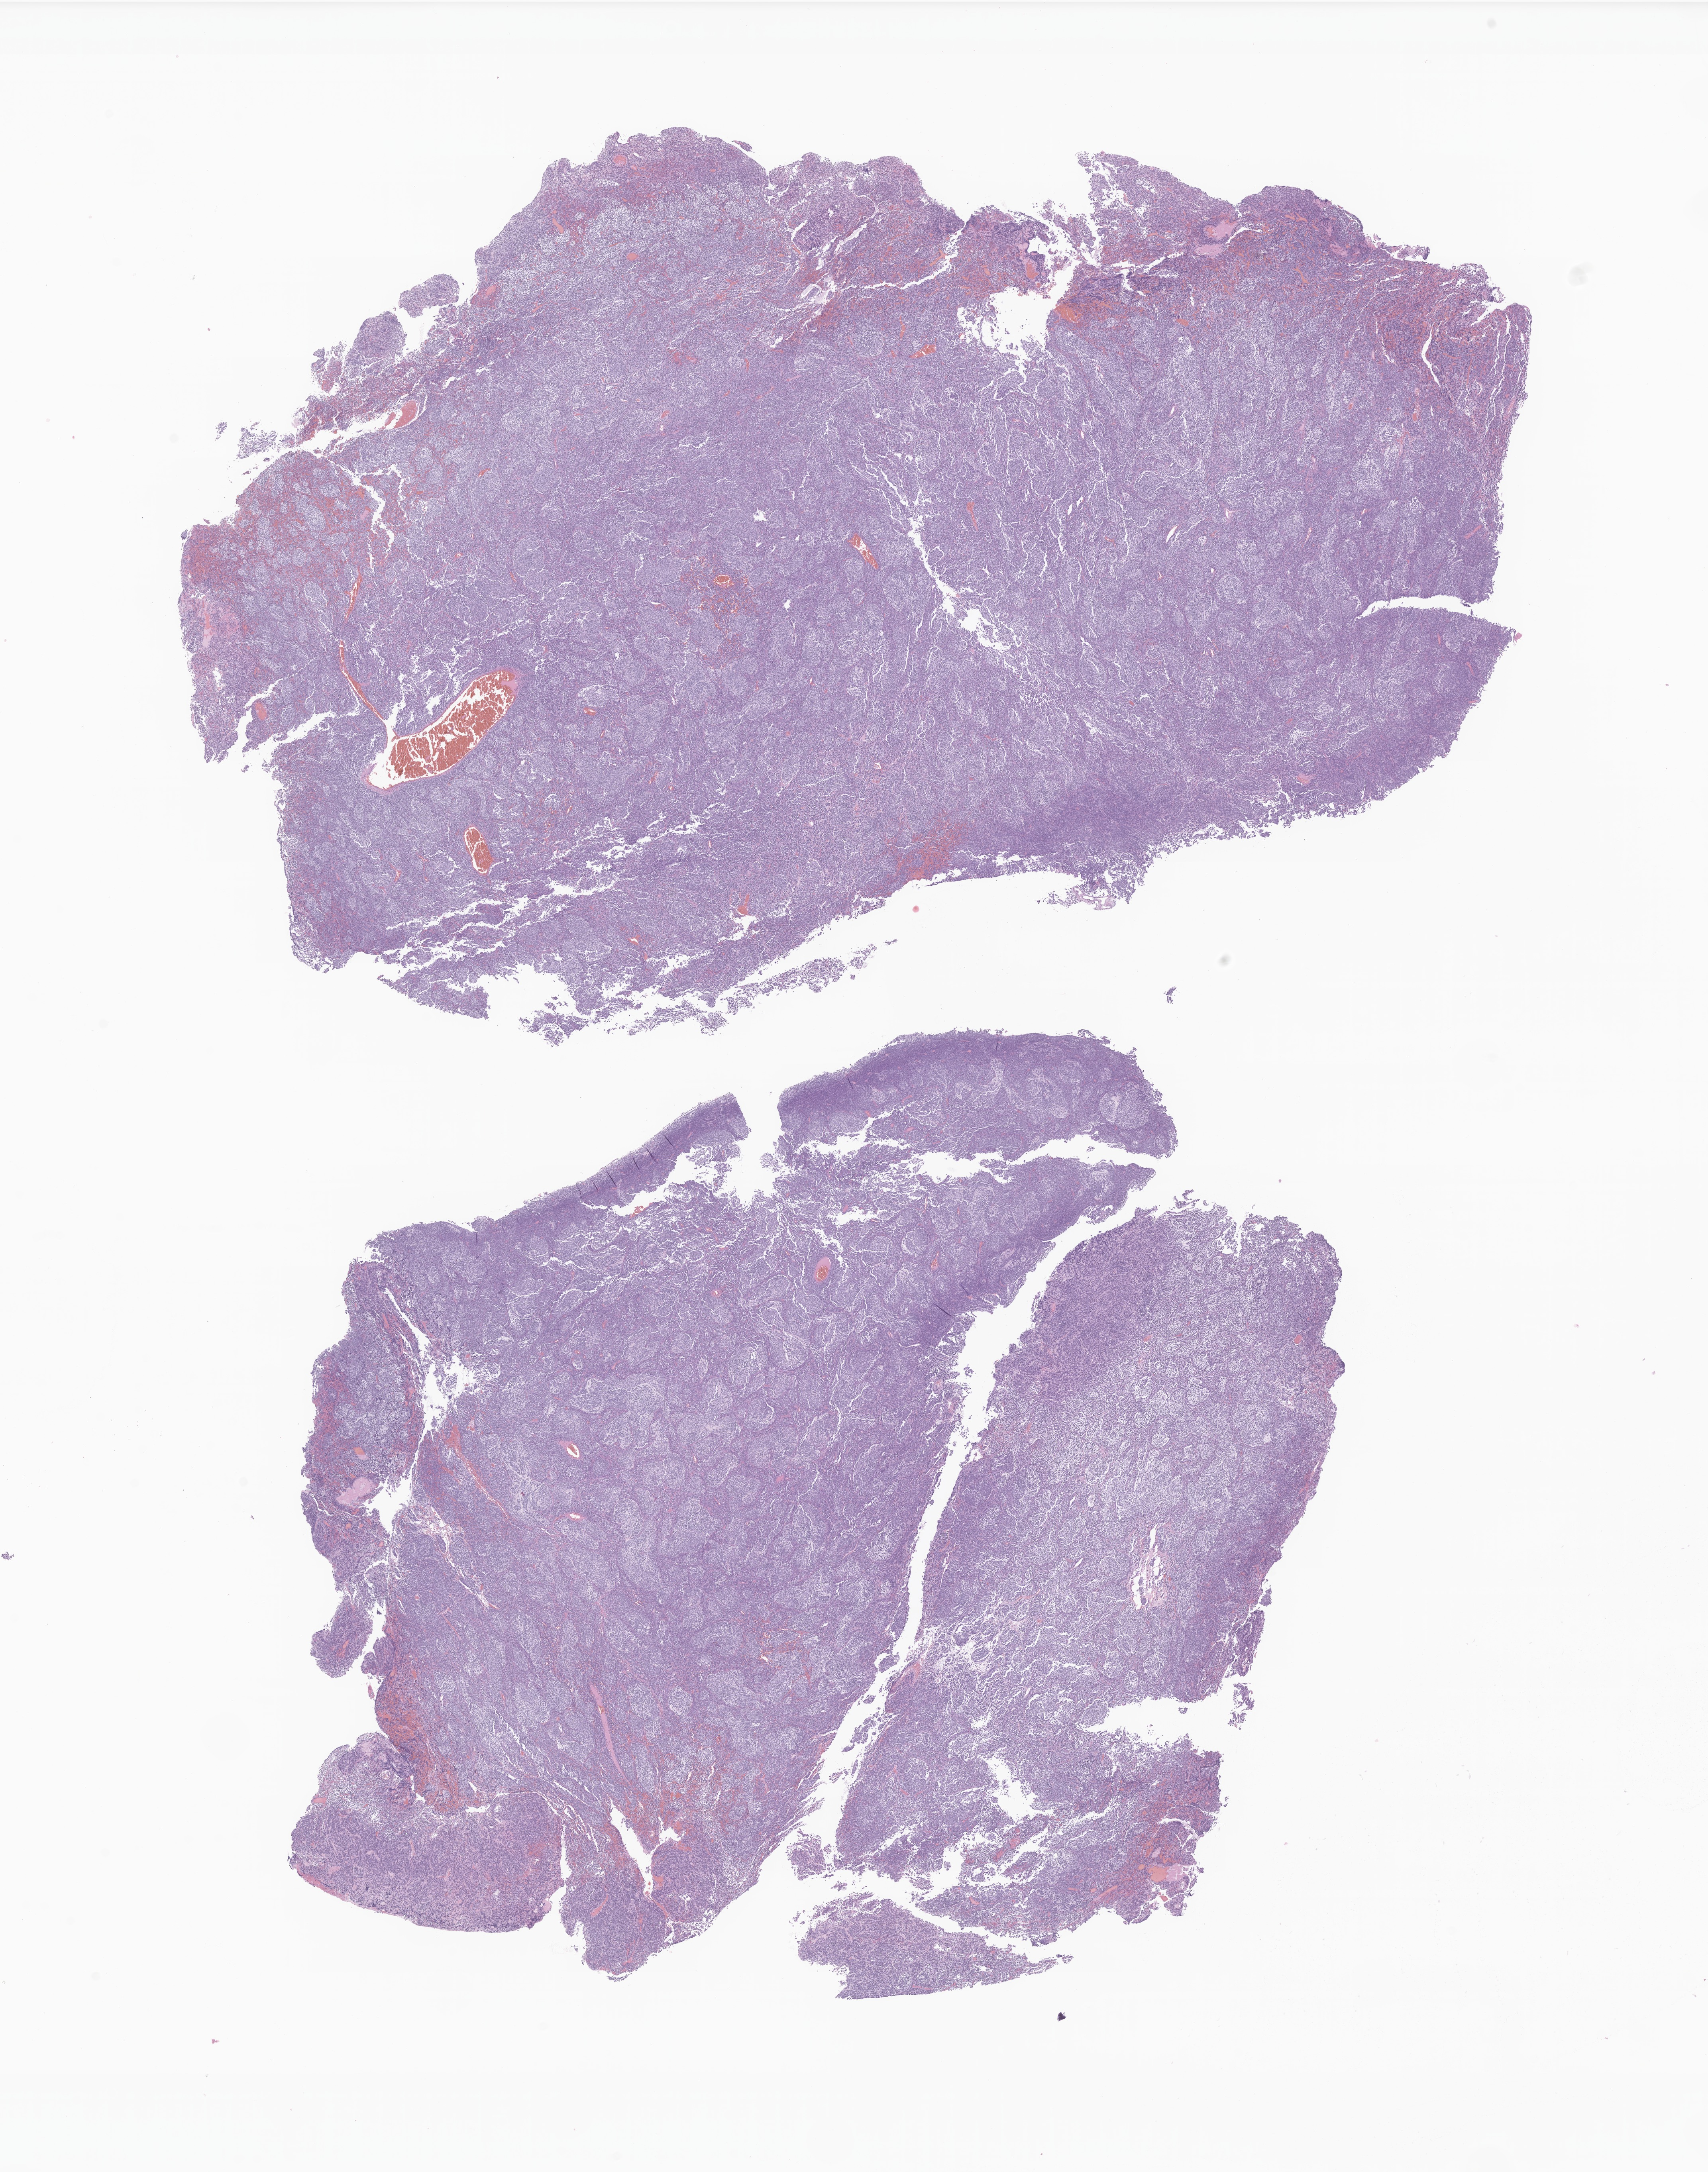
Hematoxylin and eosin (H&E) whole-slide image of tumor tissue from the brain, shown as a low-resolution overview of the whole scanned area (about 18.1 x 23.0 mm), FFPE section. Patient: male, age 52 months (4 years 4 months).
Diagnosis: Desmoplastic nodular medulloblastoma.